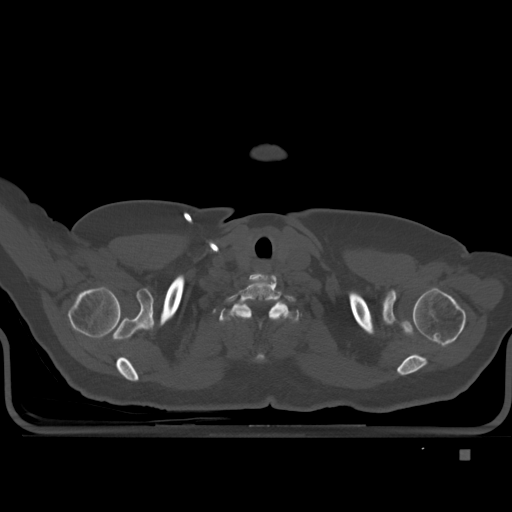
CT including the spine, one axial slice. Position 408 of 477 along the scan axis. Bone window (W 1800 / L 400 HU). 1.5 mm slice thickness. 512 × 512 image matrix, field of view 422 × 422 mm. Patient: female, 74 years. From the clinical record (not read from this slice): primary cancer: colon.
Annotated regions visible in this slice (semi-automatic segmentation, software-assisted and operator-edited):
- T1 vertebra: bounding box [x1, y1, x2, y2] px = [232, 302, 291, 360]